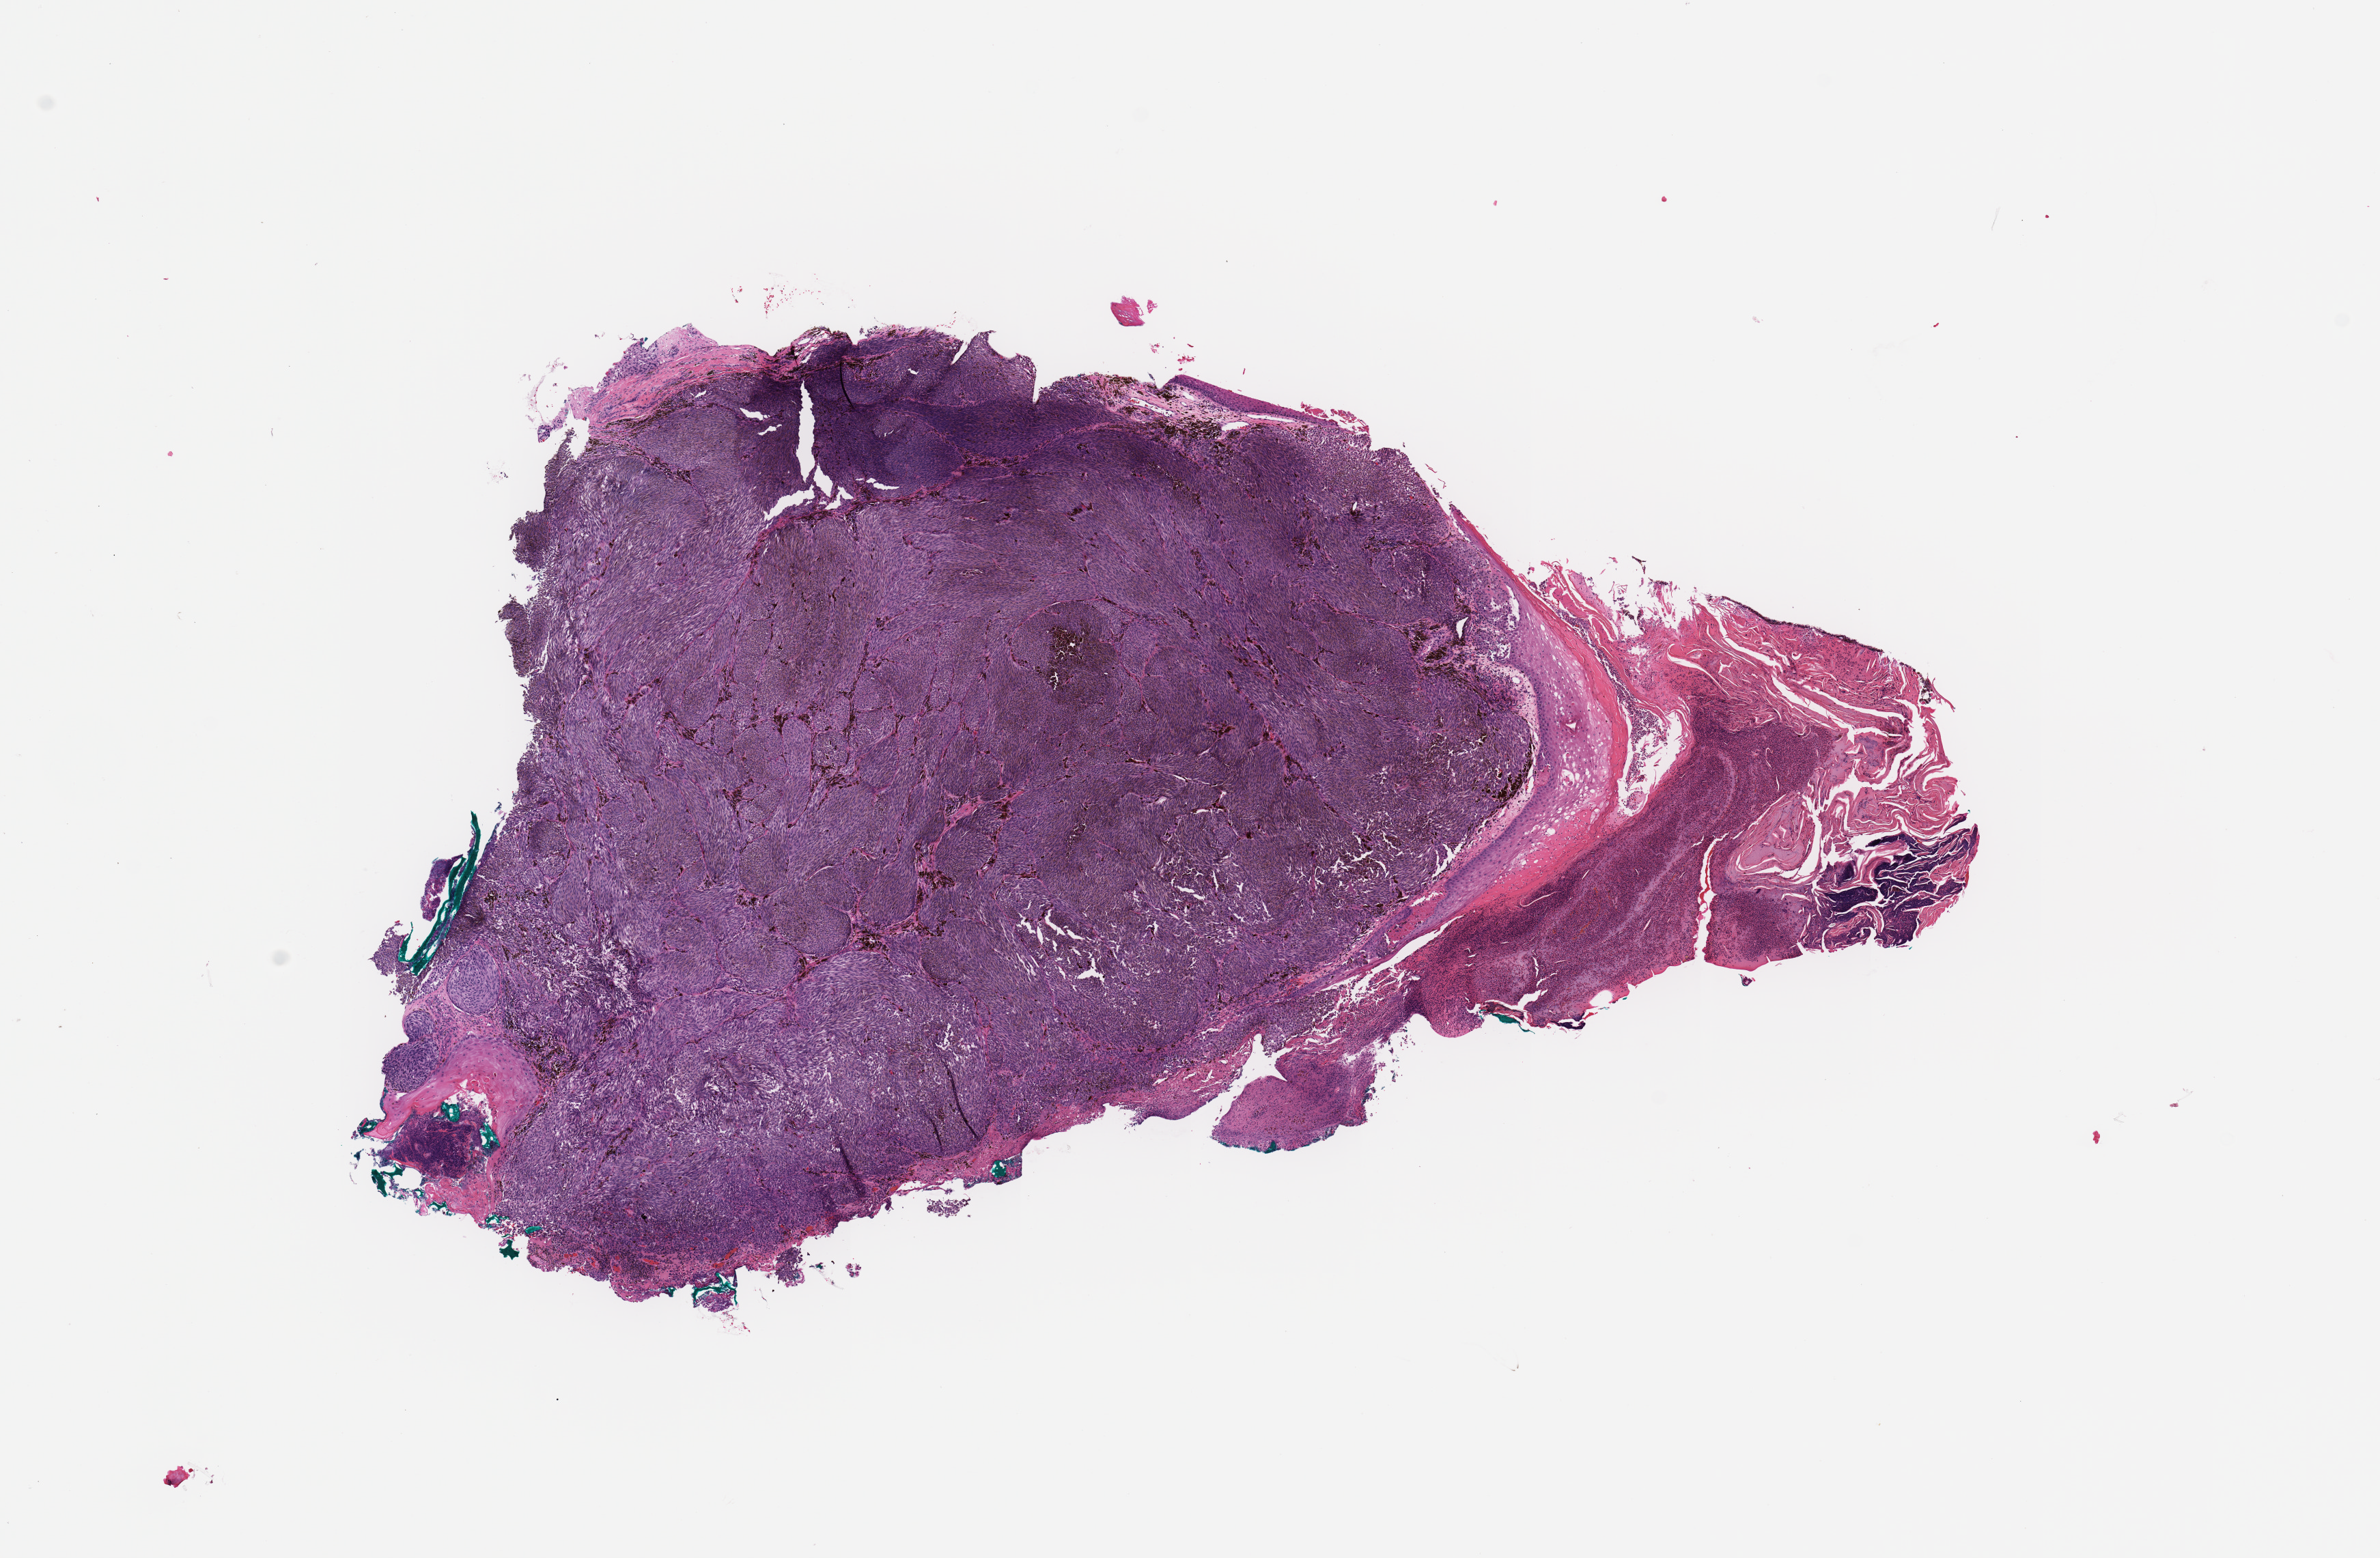
H&E whole-slide image — low-resolution overview of the scanned area, about 13.8 x 9.0 mm (slide scanned at 20x). Melanoma tumour tissue; sampled site not recorded. 78-year-old male patient.
Histologic diagnosis: Malignant melanoma, NOS. AJCC pathologic stage: IIC. Primary tumour site (as recorded): trunk.